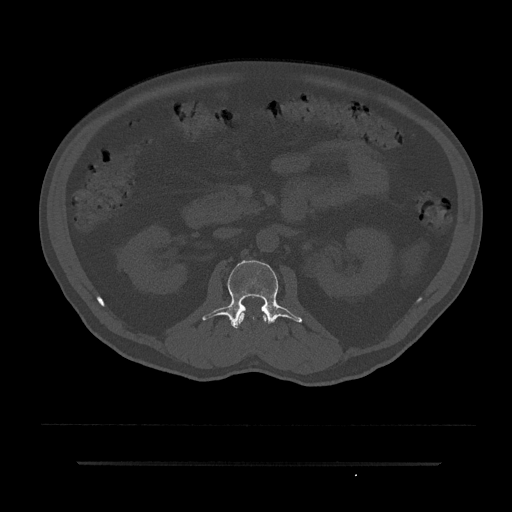
CT including the spine, one axial slice. Position 87 of 797 along the scan axis. Bone window (W 1800 / L 400 HU). 512 × 512 image matrix, field of view 464 × 464 mm. Male patient, age 59 years. From the clinical record (not read from this slice): primary cancer: bile ducts; vertebrae with lytic lesions (as recorded): T10.
Structures marked on this image (semi-automatically segmented with operator editing):
- L1 vertebra: bounding box <237,311,268,325> (left, top, right, bottom; pixels)
- L2 vertebra: <202,260,302,328>